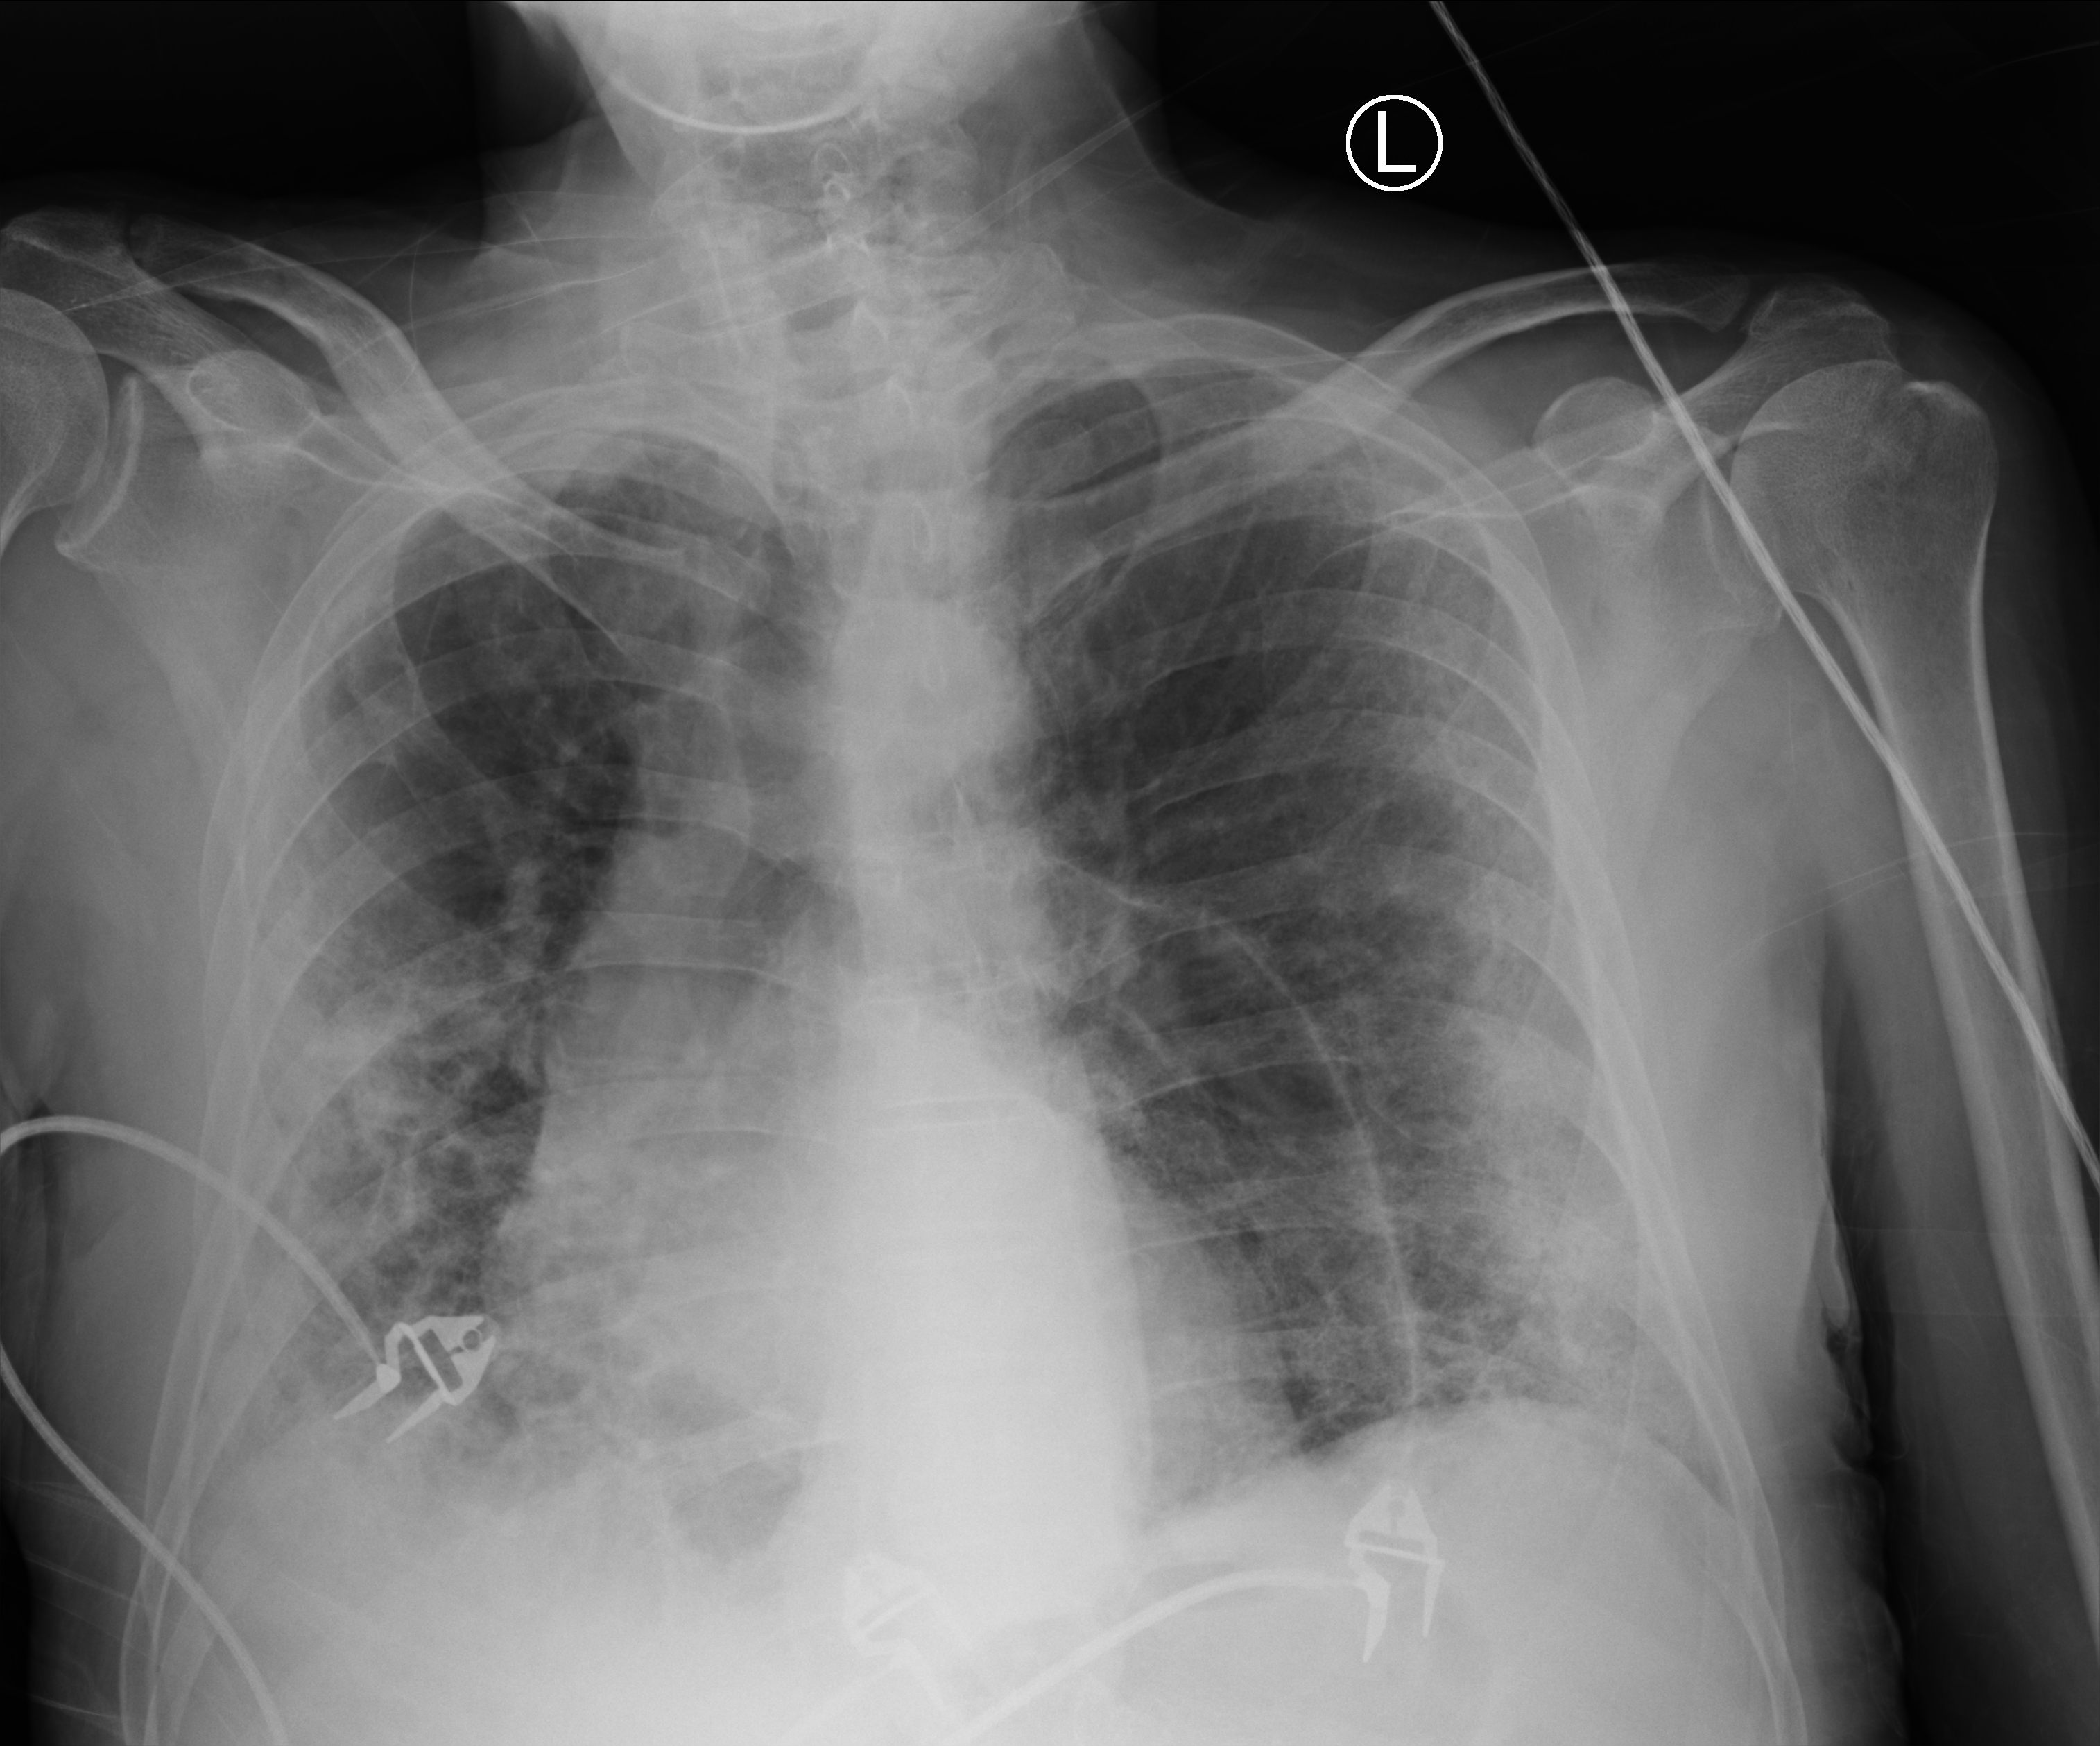
Chest X-ray (portable), anteroposterior (AP) projection. Patient hospitalised with COVID-19; male, aged 60–74 years.
From the hospital-stay record, not from the radiograph (when in the stay this image was taken is not recorded): length of hospital stay: 18 days.